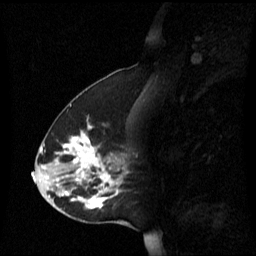
Breast MRI (dynamic contrast-enhanced), one sagittal slice; slice 26 of 60 in the series (ordered by position); dynamic contrast-enhanced series, image 2 of 3 at this slice position (ordered by acquisition); 1.5 T; TE 4.2 ms, TR 8.4 ms; 2.2 mm slice thickness; 256 × 256 image matrix, field of view 240 × 240 mm. Patient: female, 45 years. Case-level facts recorded for this patient, not image findings: setting: breast cancer imaged before/during neoadjuvant chemotherapy; receptor status: HR-positive, HER2-negative.
Outlined on this slice (semi-automatic segmentation, software-assisted and operator-edited):
- analysis volume of interest (the breast-tissue region the enhancement analysis was run in; not a lesion): bounding box [x1, y1, x2, y2] px = [38, 124, 129, 221]
- tumour enhancement mask (voxels above the 70 % enhancement threshold inside the analysis volume of interest): [58, 126, 119, 209]